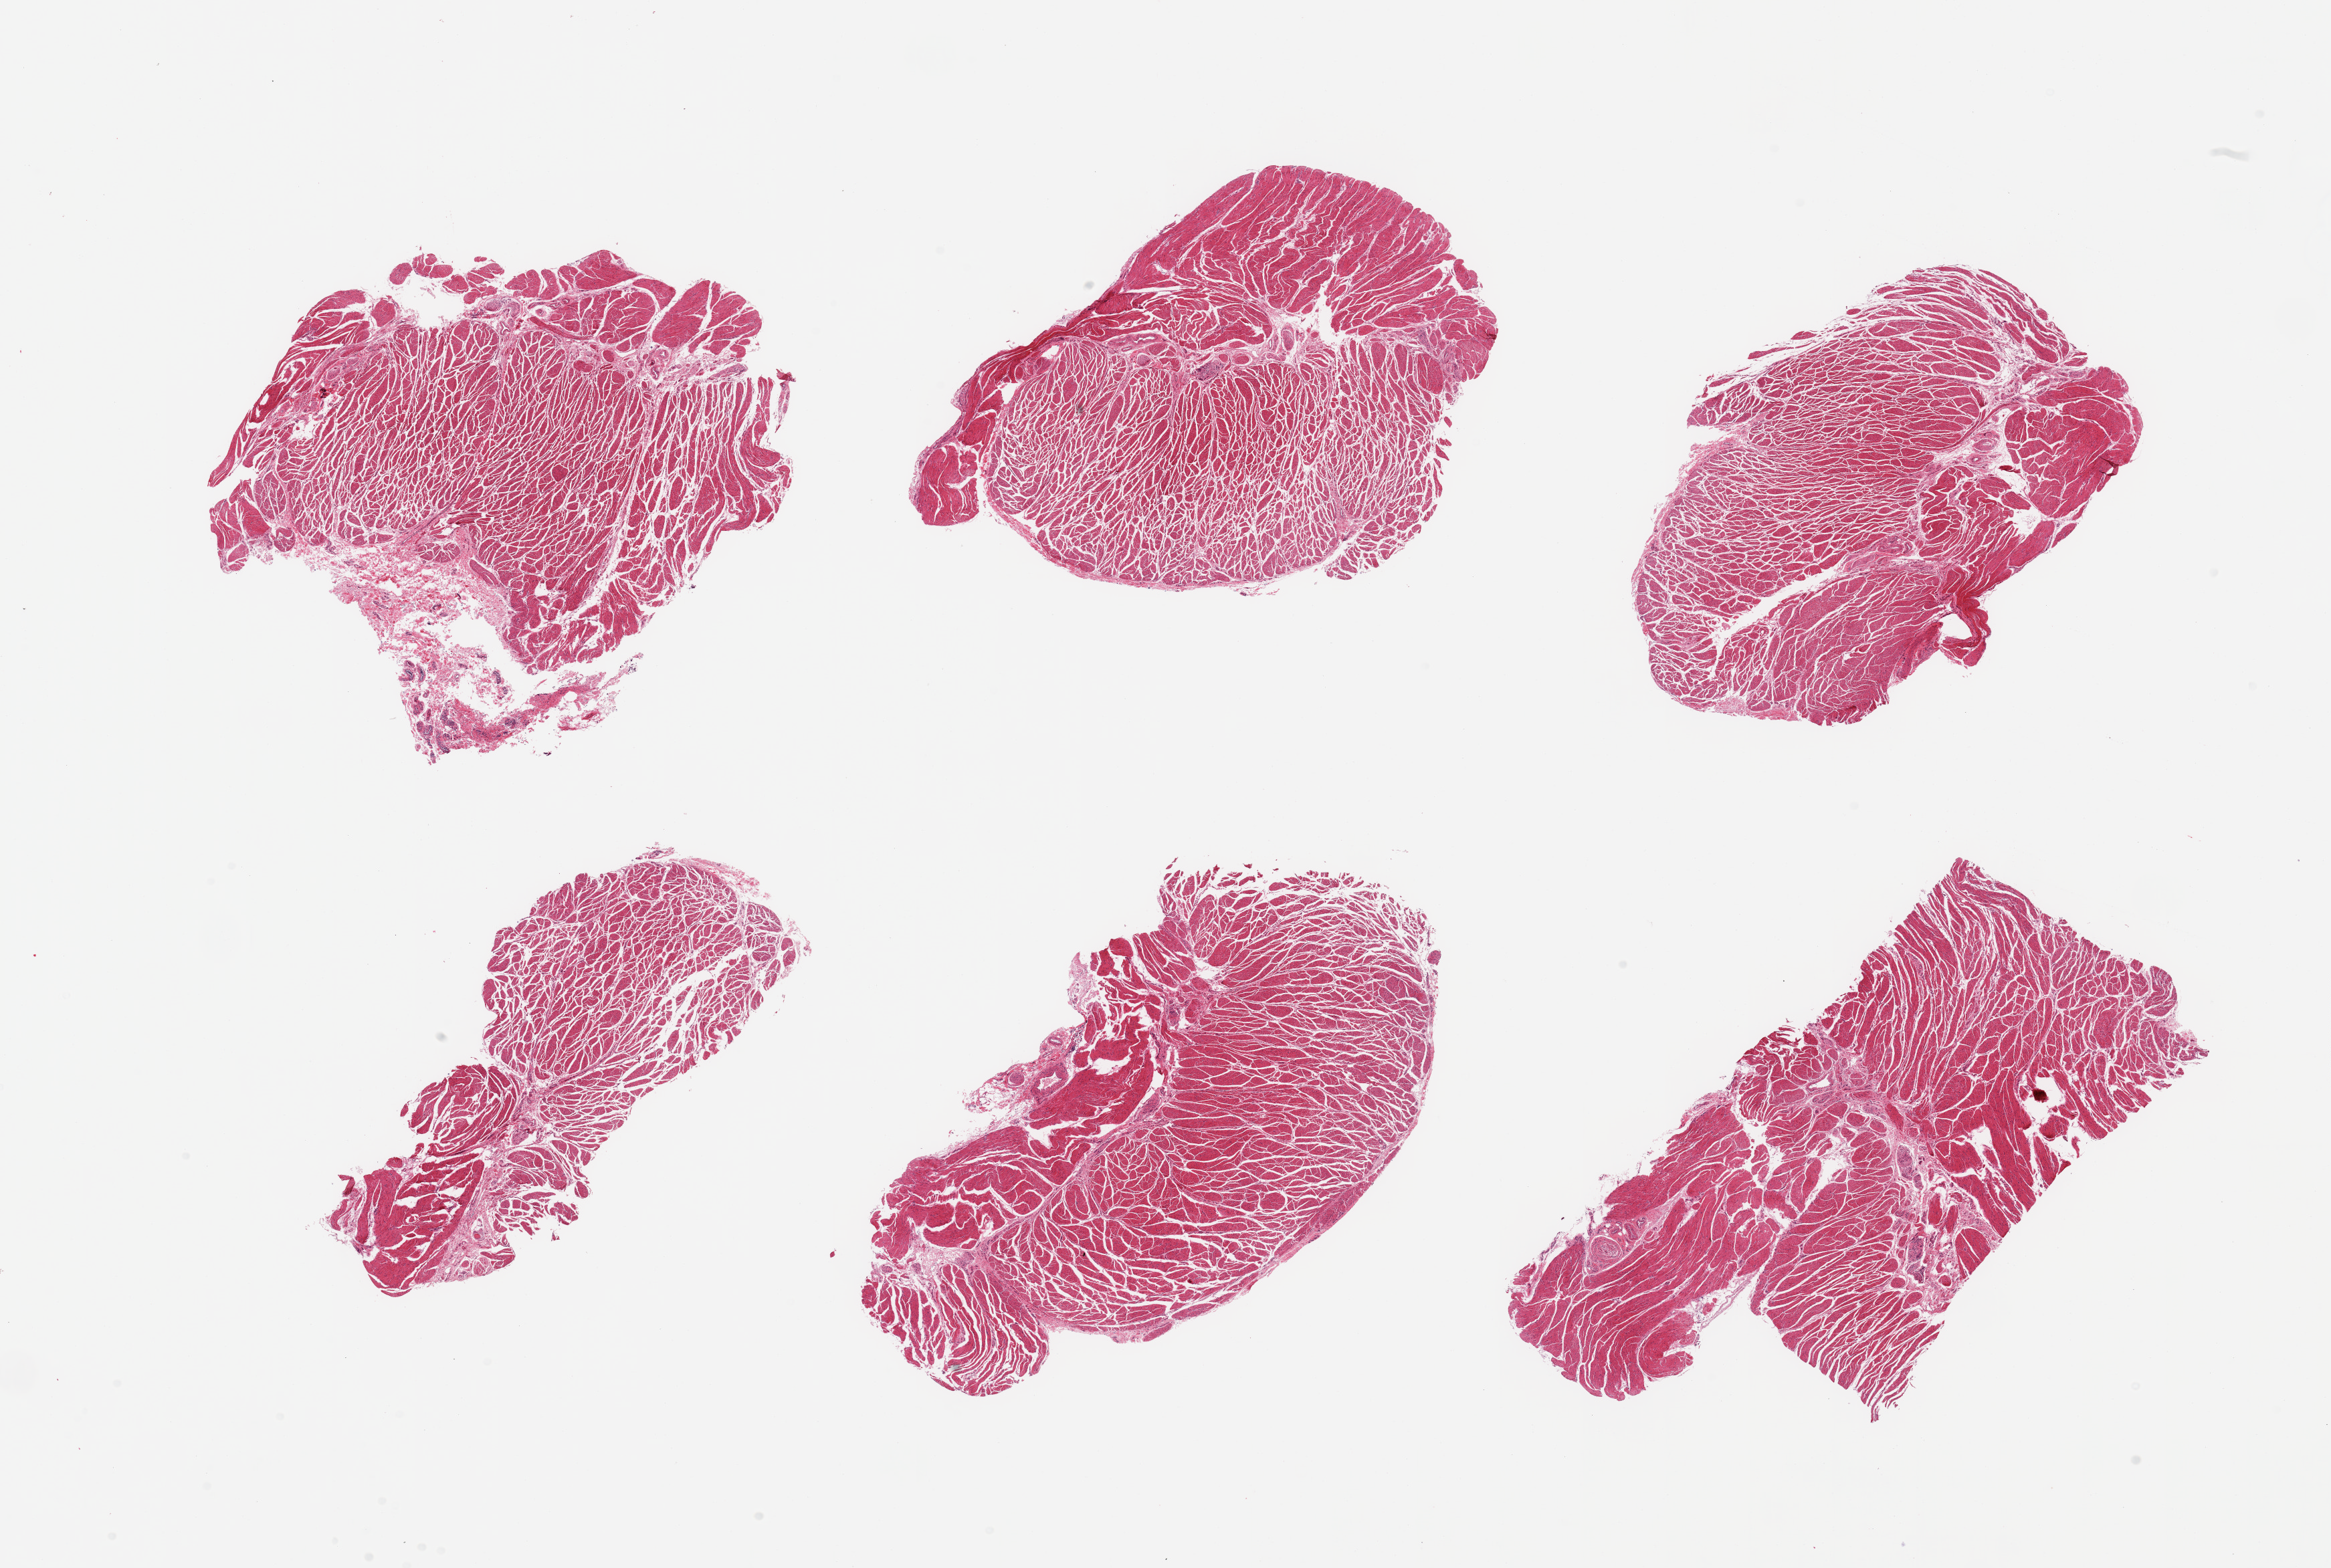
Digitized H&E-stained section, brightfield, a low-resolution overview of the entire scanned area, about 27.6 x 18.5 mm (slide scanned at 20x), PAXgene-fixed paraffin-embedded (PFPE) section, section of esophageal muscle (target tissue), tissue donor sample.
Reviewer comment on this tissue sample: 6 pieces; target muscularis.